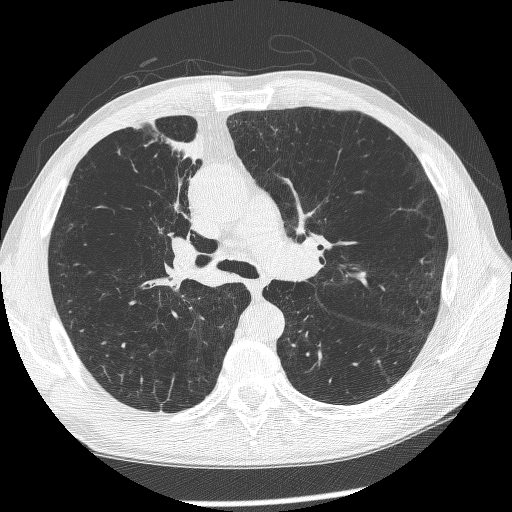
Low-dose screening chest CT, axial slice. First (baseline) screen. Lung window (W 1500 / L -600 HU). 1.25 mm slice thickness. Slice 155 of 266 in the series. 512 × 512 image matrix. Male participant, aged 60 years at enrolment.
- Expert reader's lesion annotation, bounding box (x1, y1, x2, y2) in pixels: (144, 204, 224, 296).
- Screening reader's record for this exam (one nodule recorded; not confirmed to be the boxed lesion): non-calcified nodule or mass ≥4 mm, right upper lobe, 12 × 8 mm, spiculated (stellate) margins, mixed attenuation.
- Official screen result: positive, change unspecified: nodule(s) >= 4 mm or enlarging nodule(s), mass(es), or other non-specific abnormalities suspicious for lung cancer.